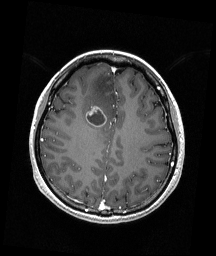
Brain MRI from a brain-tumour surgery series, one axial slice; position 64 of 192 along the scan axis; T1-weighted post-contrast; 1 mm slice thickness; 216 × 256 image matrix, field of view 211 × 250 mm. From the clinical record (not read from this slice): histopathology: Astrocytoma; WHO grade: 4; IDH mutation: yes; tumour location: Right Frontal.
Structures marked on this image (manually delineated by an expert):
- tumour: bounding box <86,106,106,127> (left, top, right, bottom; pixels)